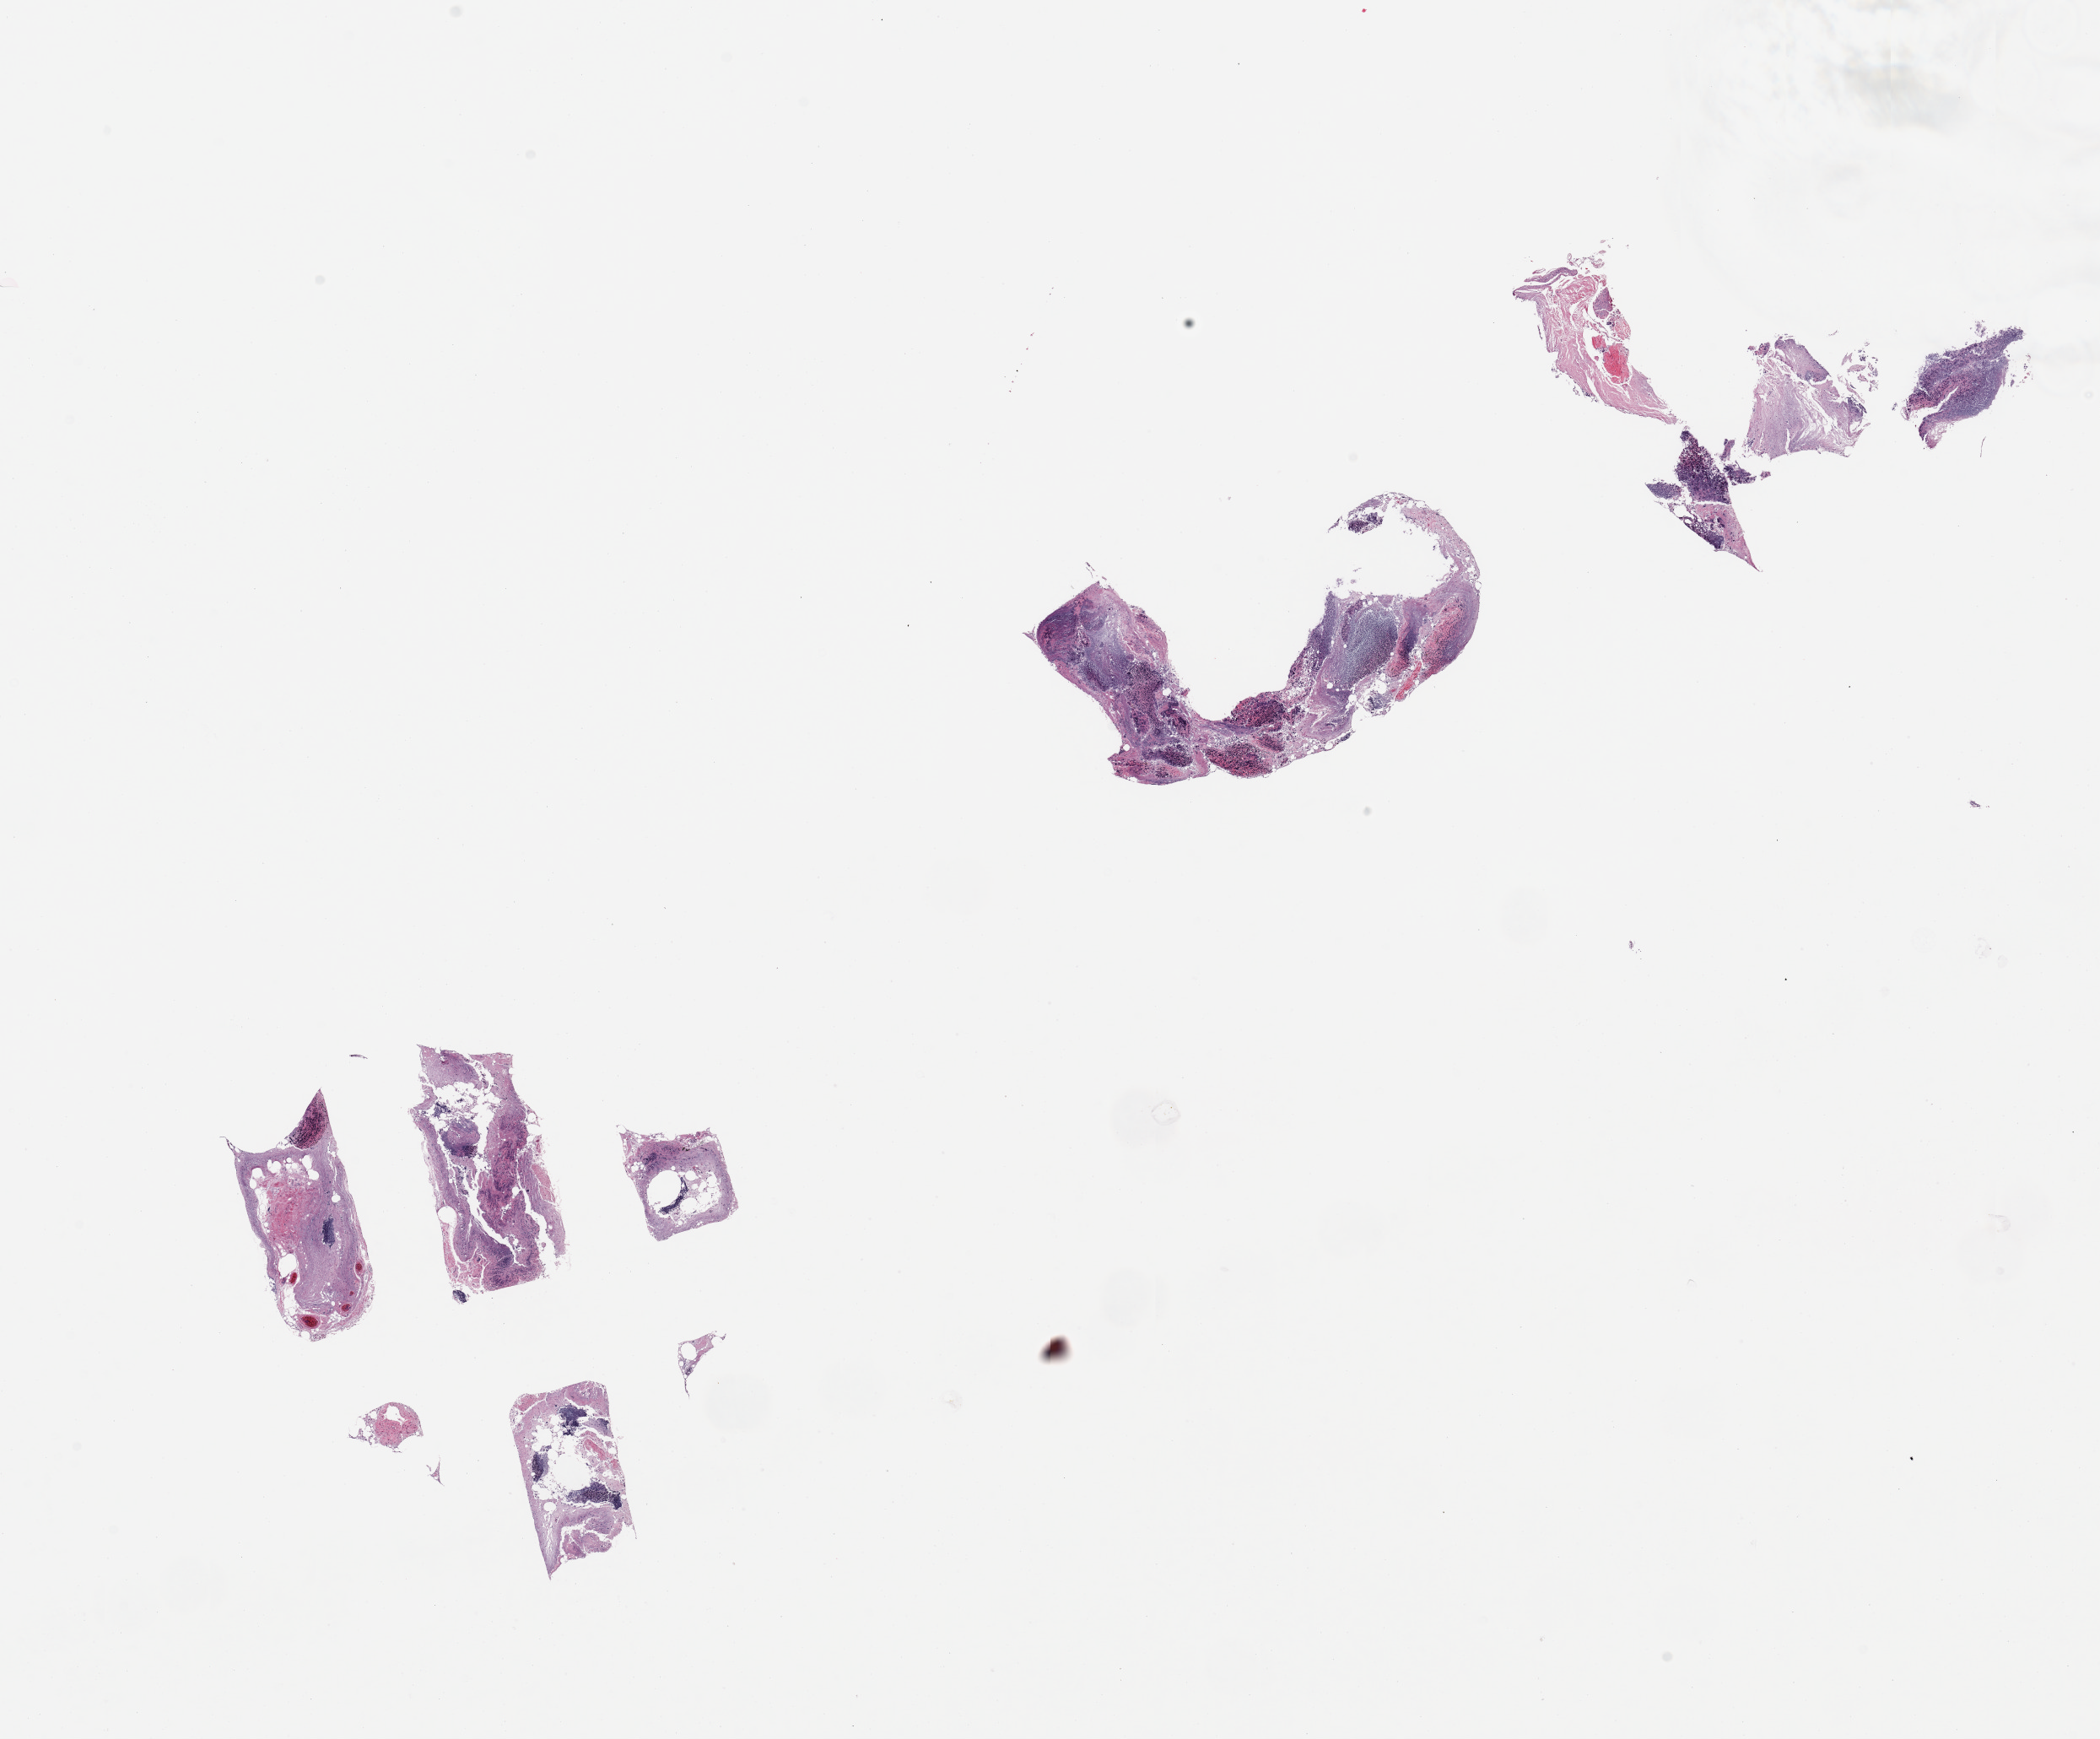
Hematoxylin and eosin (H&E) whole-slide image — low-resolution overview of the scanned area, about 19.7 x 16.3 mm (slide scanned at 20x); PAXgene-fixed, paraffin-embedded tissue; section of ileum (target tissue); tissue donor sample. Male donor.
Reviewer comment on this tissue sample: 6 fragmented pieces; lymphoid tissue autolyzed.